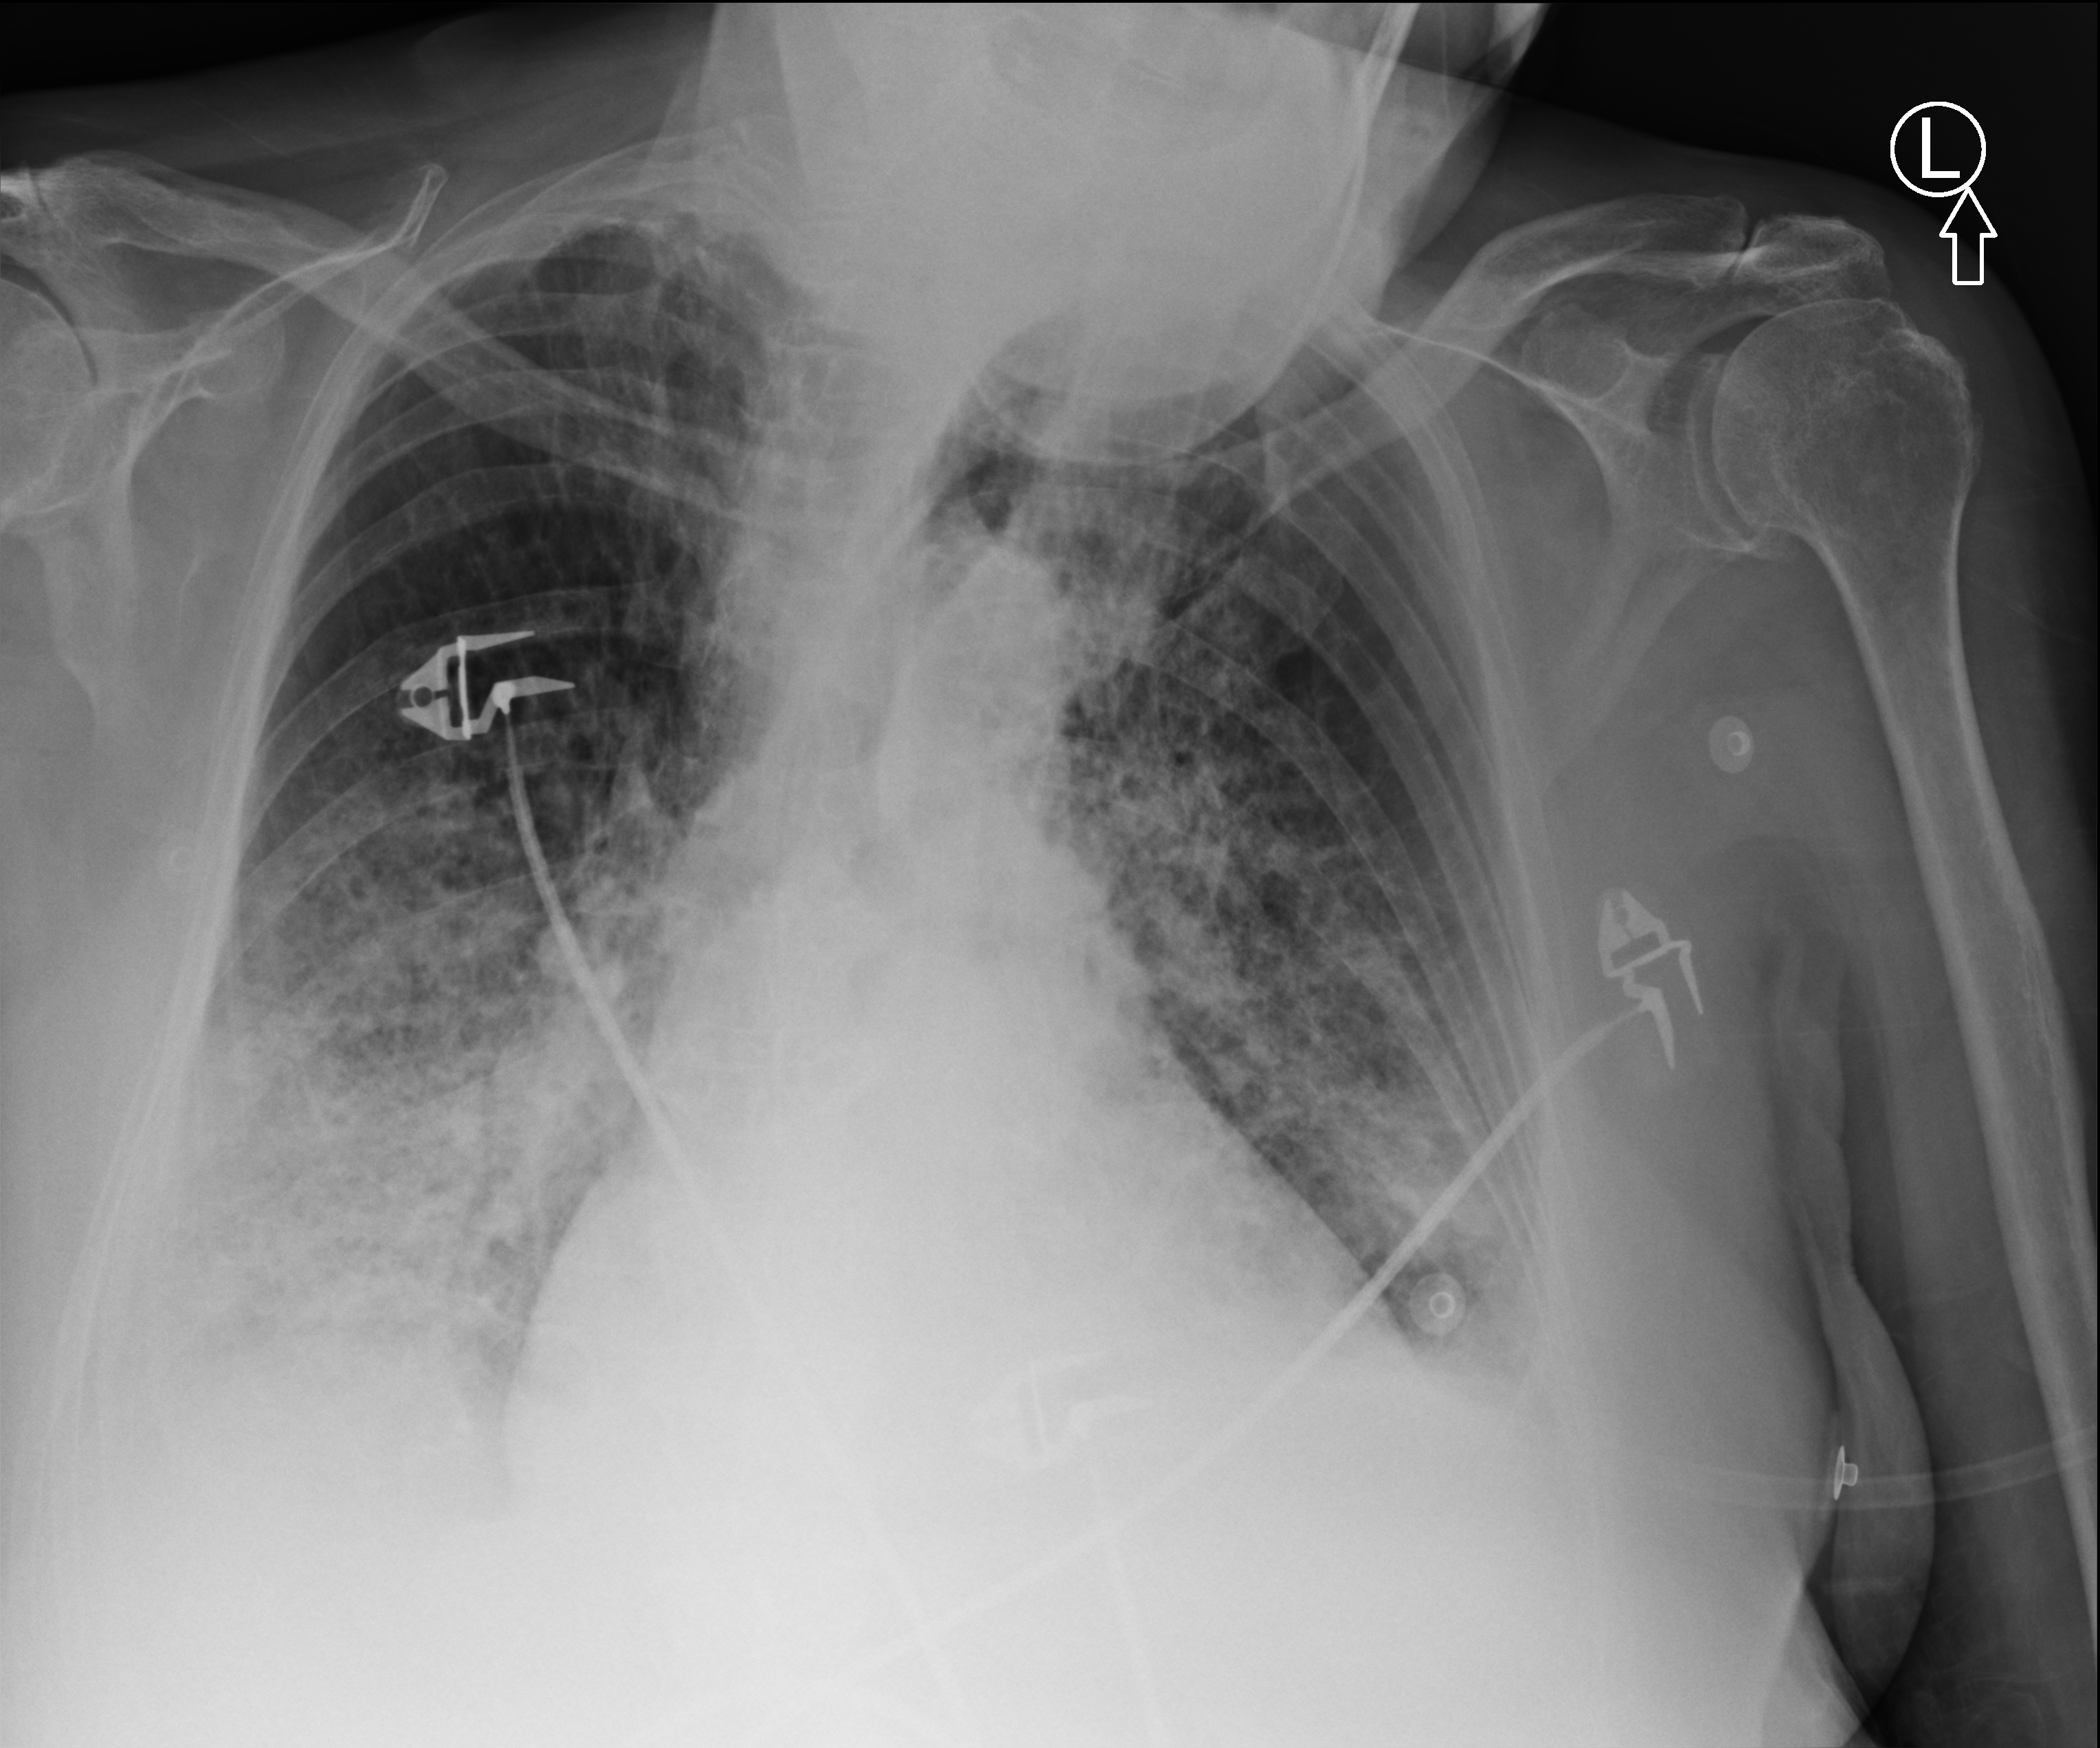
Portable chest radiograph, anteroposterior (AP) projection. Patient hospitalised with COVID-19; male, aged 75–90 years.
Admission-level facts for this patient (not findings on this image; timing relative to this image not recorded): COPD (admission record): yes; admitted to intensive care during this hospital stay: no.